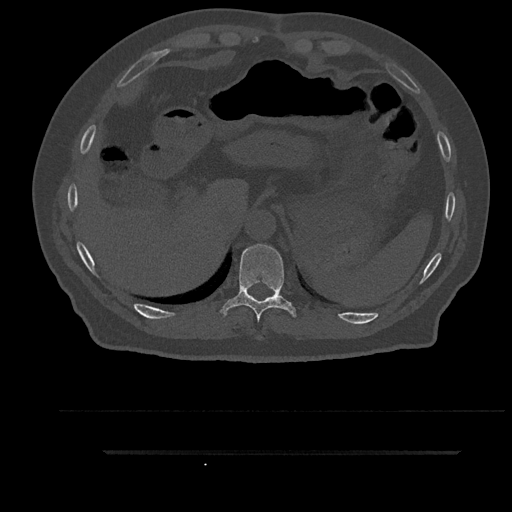
CT including the spine, one axial slice. Slice 363 of 797 in the series (ordered by position). Reconstruction kernel Br40s/3. Bone window (W 1800 / L 400 HU). 0.5 mm slice thickness. 512 × 512 image matrix, field of view 432 × 432 mm. Male patient, age 63 years. From the clinical record (not read from this slice): primary cancer: renal.
Outlined on this slice (semi-automatic segmentation, software-assisted and operator-edited):
- T10 vertebra: bounding box [x1, y1, x2, y2] px = [220, 244, 297, 322]